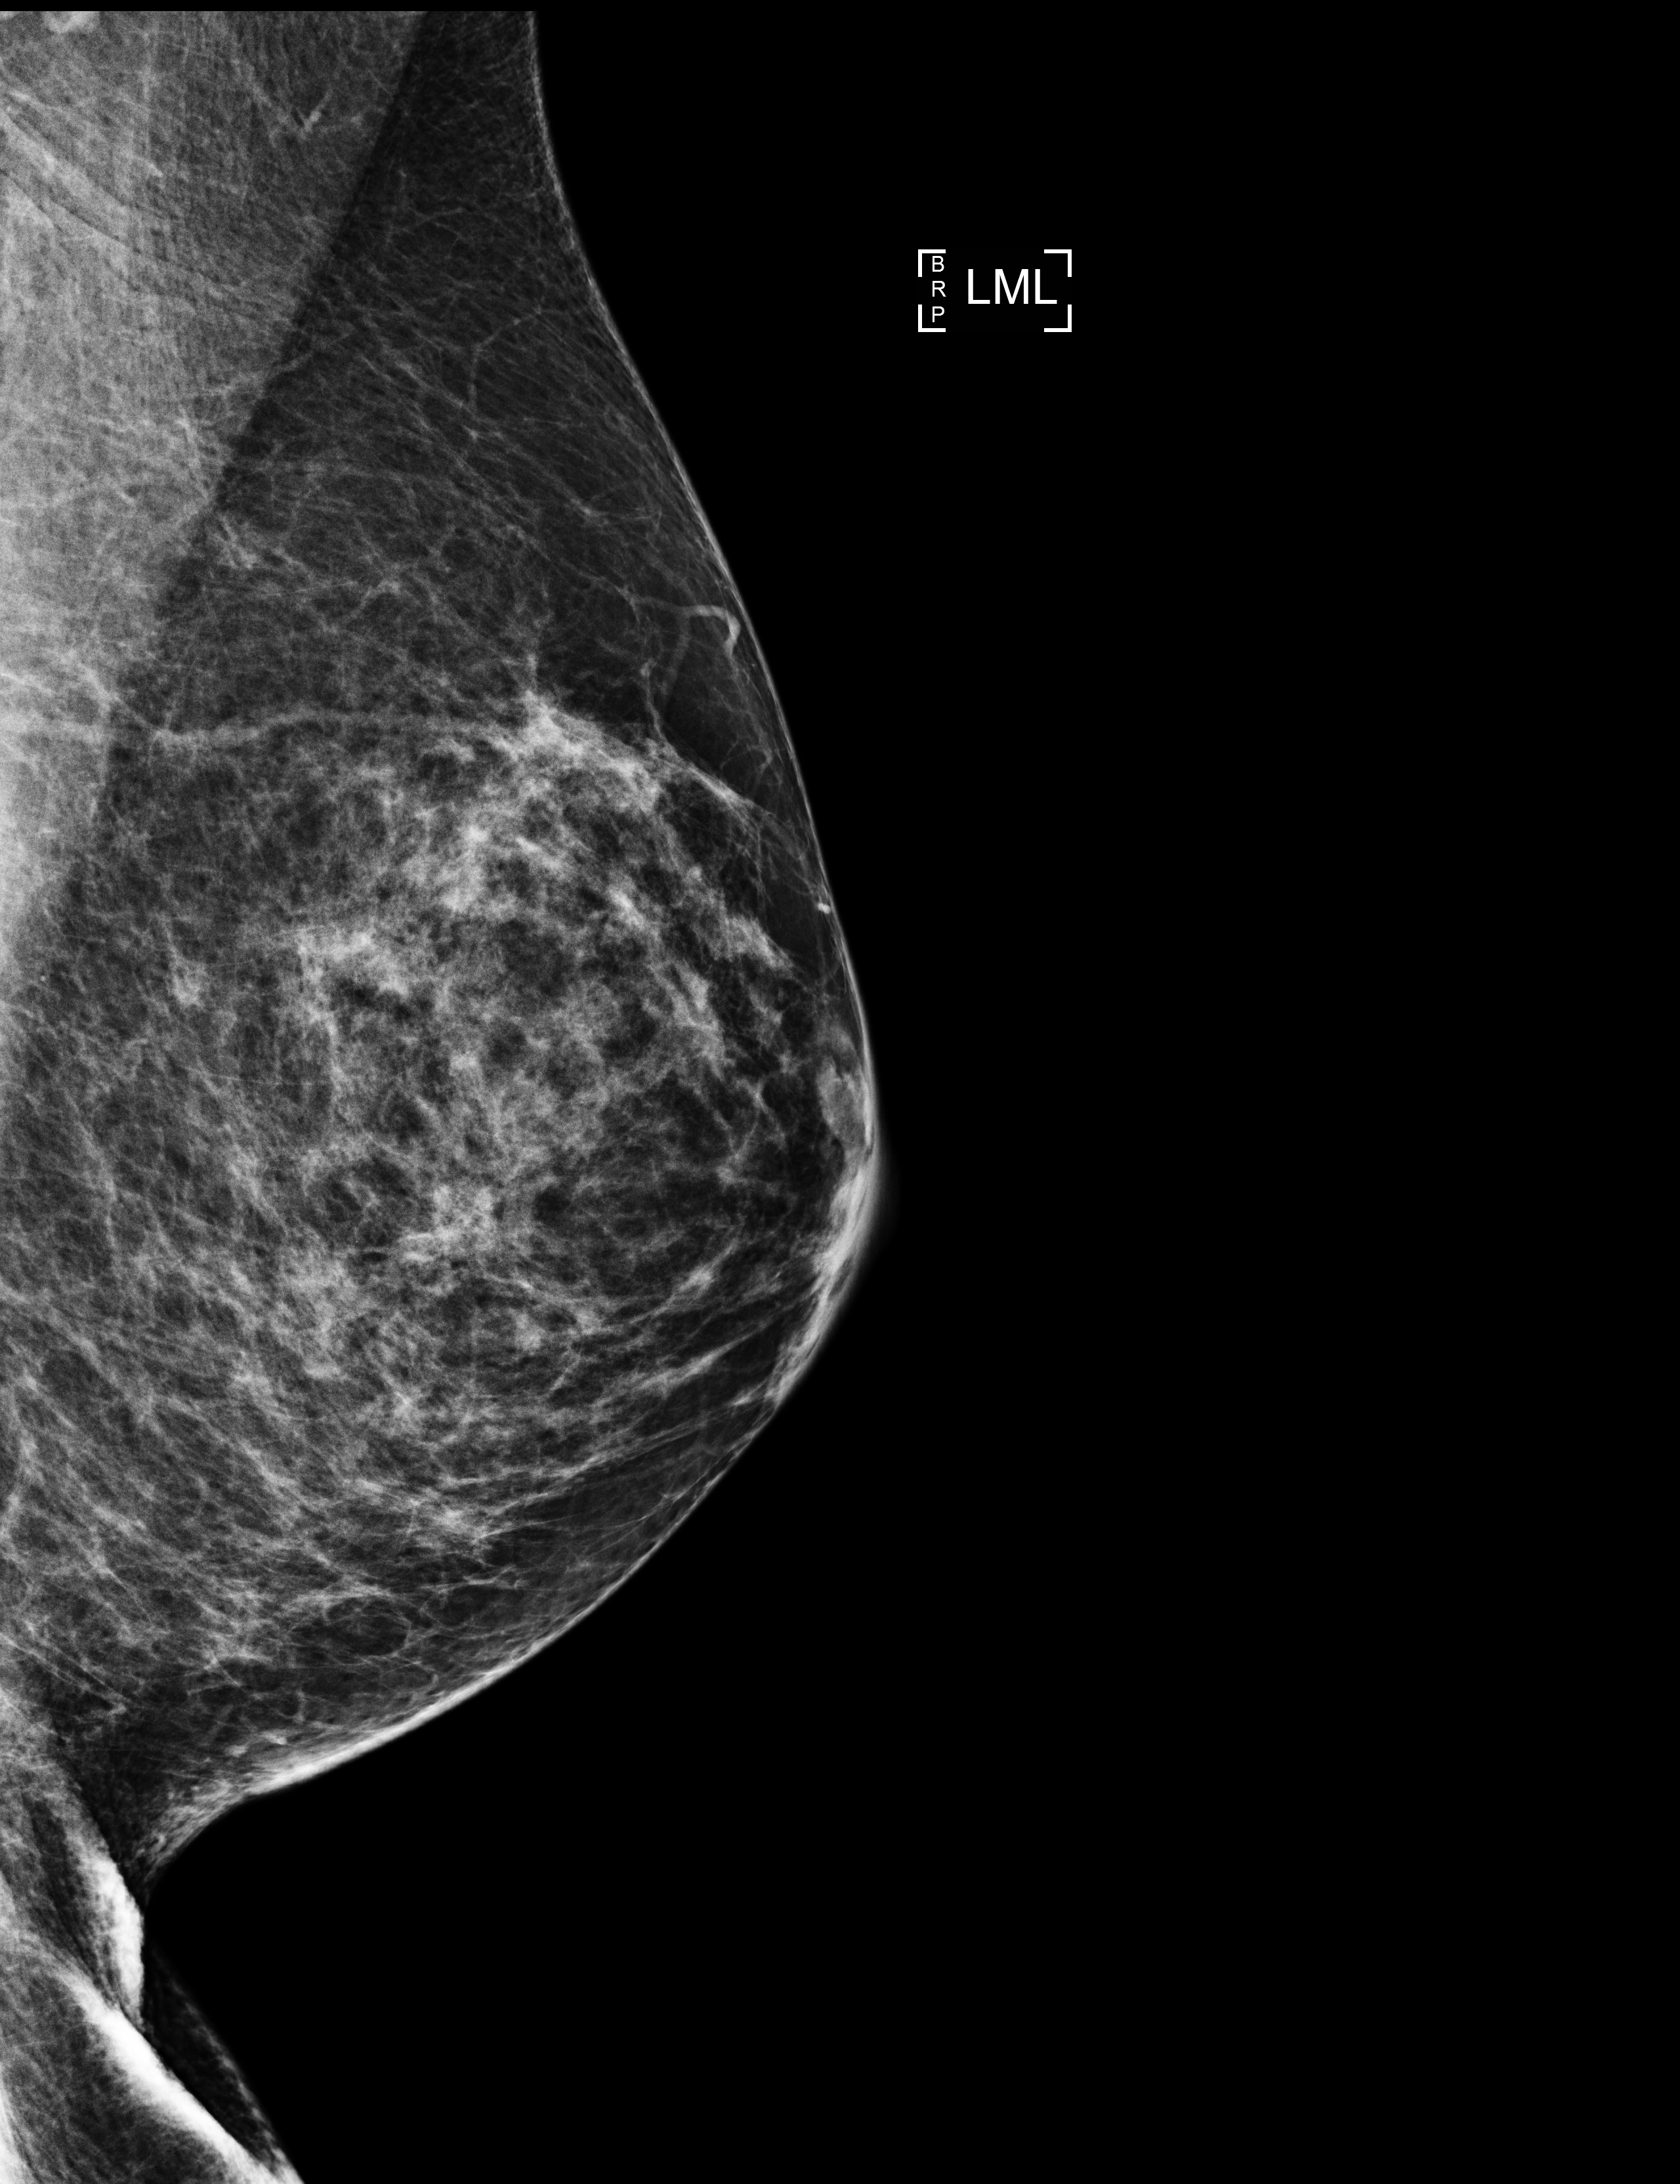
Annual screening mammography examination; compressed breast thickness 64 mm. Patient aged 63 years (female).
Image type: full-field digital mammogram. Breast: left. Projection: ML view. Breast density at the screening exam (both breasts): heterogeneously dense (BI-RADS density category c). Final BI-RADS category for the screening round (tomosynthesis exam, both breasts): category 2. Recall: no recall after this screen.